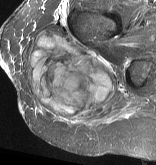
MRI of an extremity soft-tissue mass, one axial slice. STIR. MR volume resampled by the dataset authors to the PET/CT grid (not the native acquisition matrix). 3.27 mm slice thickness. 156 × 165 image matrix, field of view 152 × 161 mm. Female patient. Case-level facts recorded for this patient, not image findings: histological type: epithelioid sarcoma with vascular differentiation; site of the primary tumour: right buttock.
Structures marked on this image (expert contour drawn on MRI and transferred to this co-registered scan by the dataset authors):
- gross tumour volume (mass): bounding box <26,32,116,122> (left, top, right, bottom; pixels)